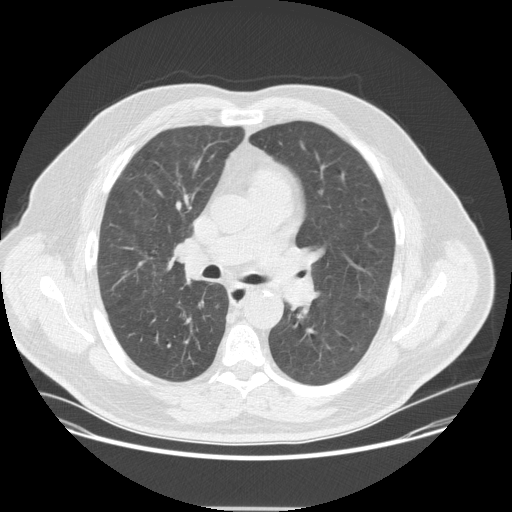
Low-dose screening chest CT, one axial slice; position 215 of 351 along the scan axis; reconstruction kernel STANDARD; 120 kVp; lung window (W 1500 / L -600 HU); 512 × 512 image matrix.
Structures marked on this image (expert manual segmentation):
- lesion 1 (tumor, upper lobe of right lung): bounding box [x1, y1, x2, y2] px = [187, 277, 190, 279]